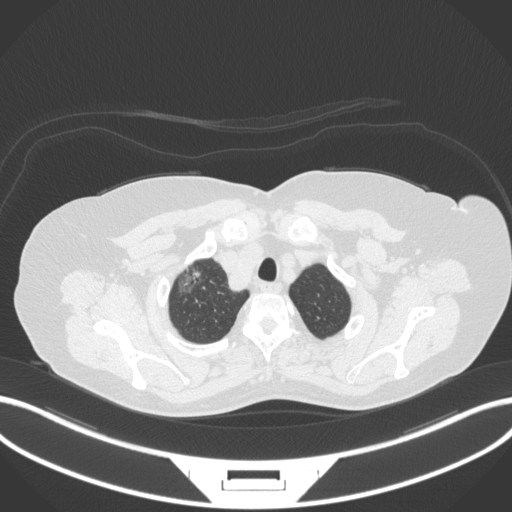
Chest CT, one axial slice. Slice 314 of 365 in the series (ordered by position). Lung window (W 1500 / L -600 HU). 1 mm slice thickness. 512 × 512 image matrix, field of view 400 × 400 mm. Female patient, age 62 years. From the clinical record (not read from this slice): clinical TNM (as recorded): T1c N0 M0.
Structures marked on this image (bounding box drawn by a radiologist):
- lung tumour (recorded histology: adenocarcinoma): bounding box <175,261,207,299> (left, top, right, bottom; pixels)